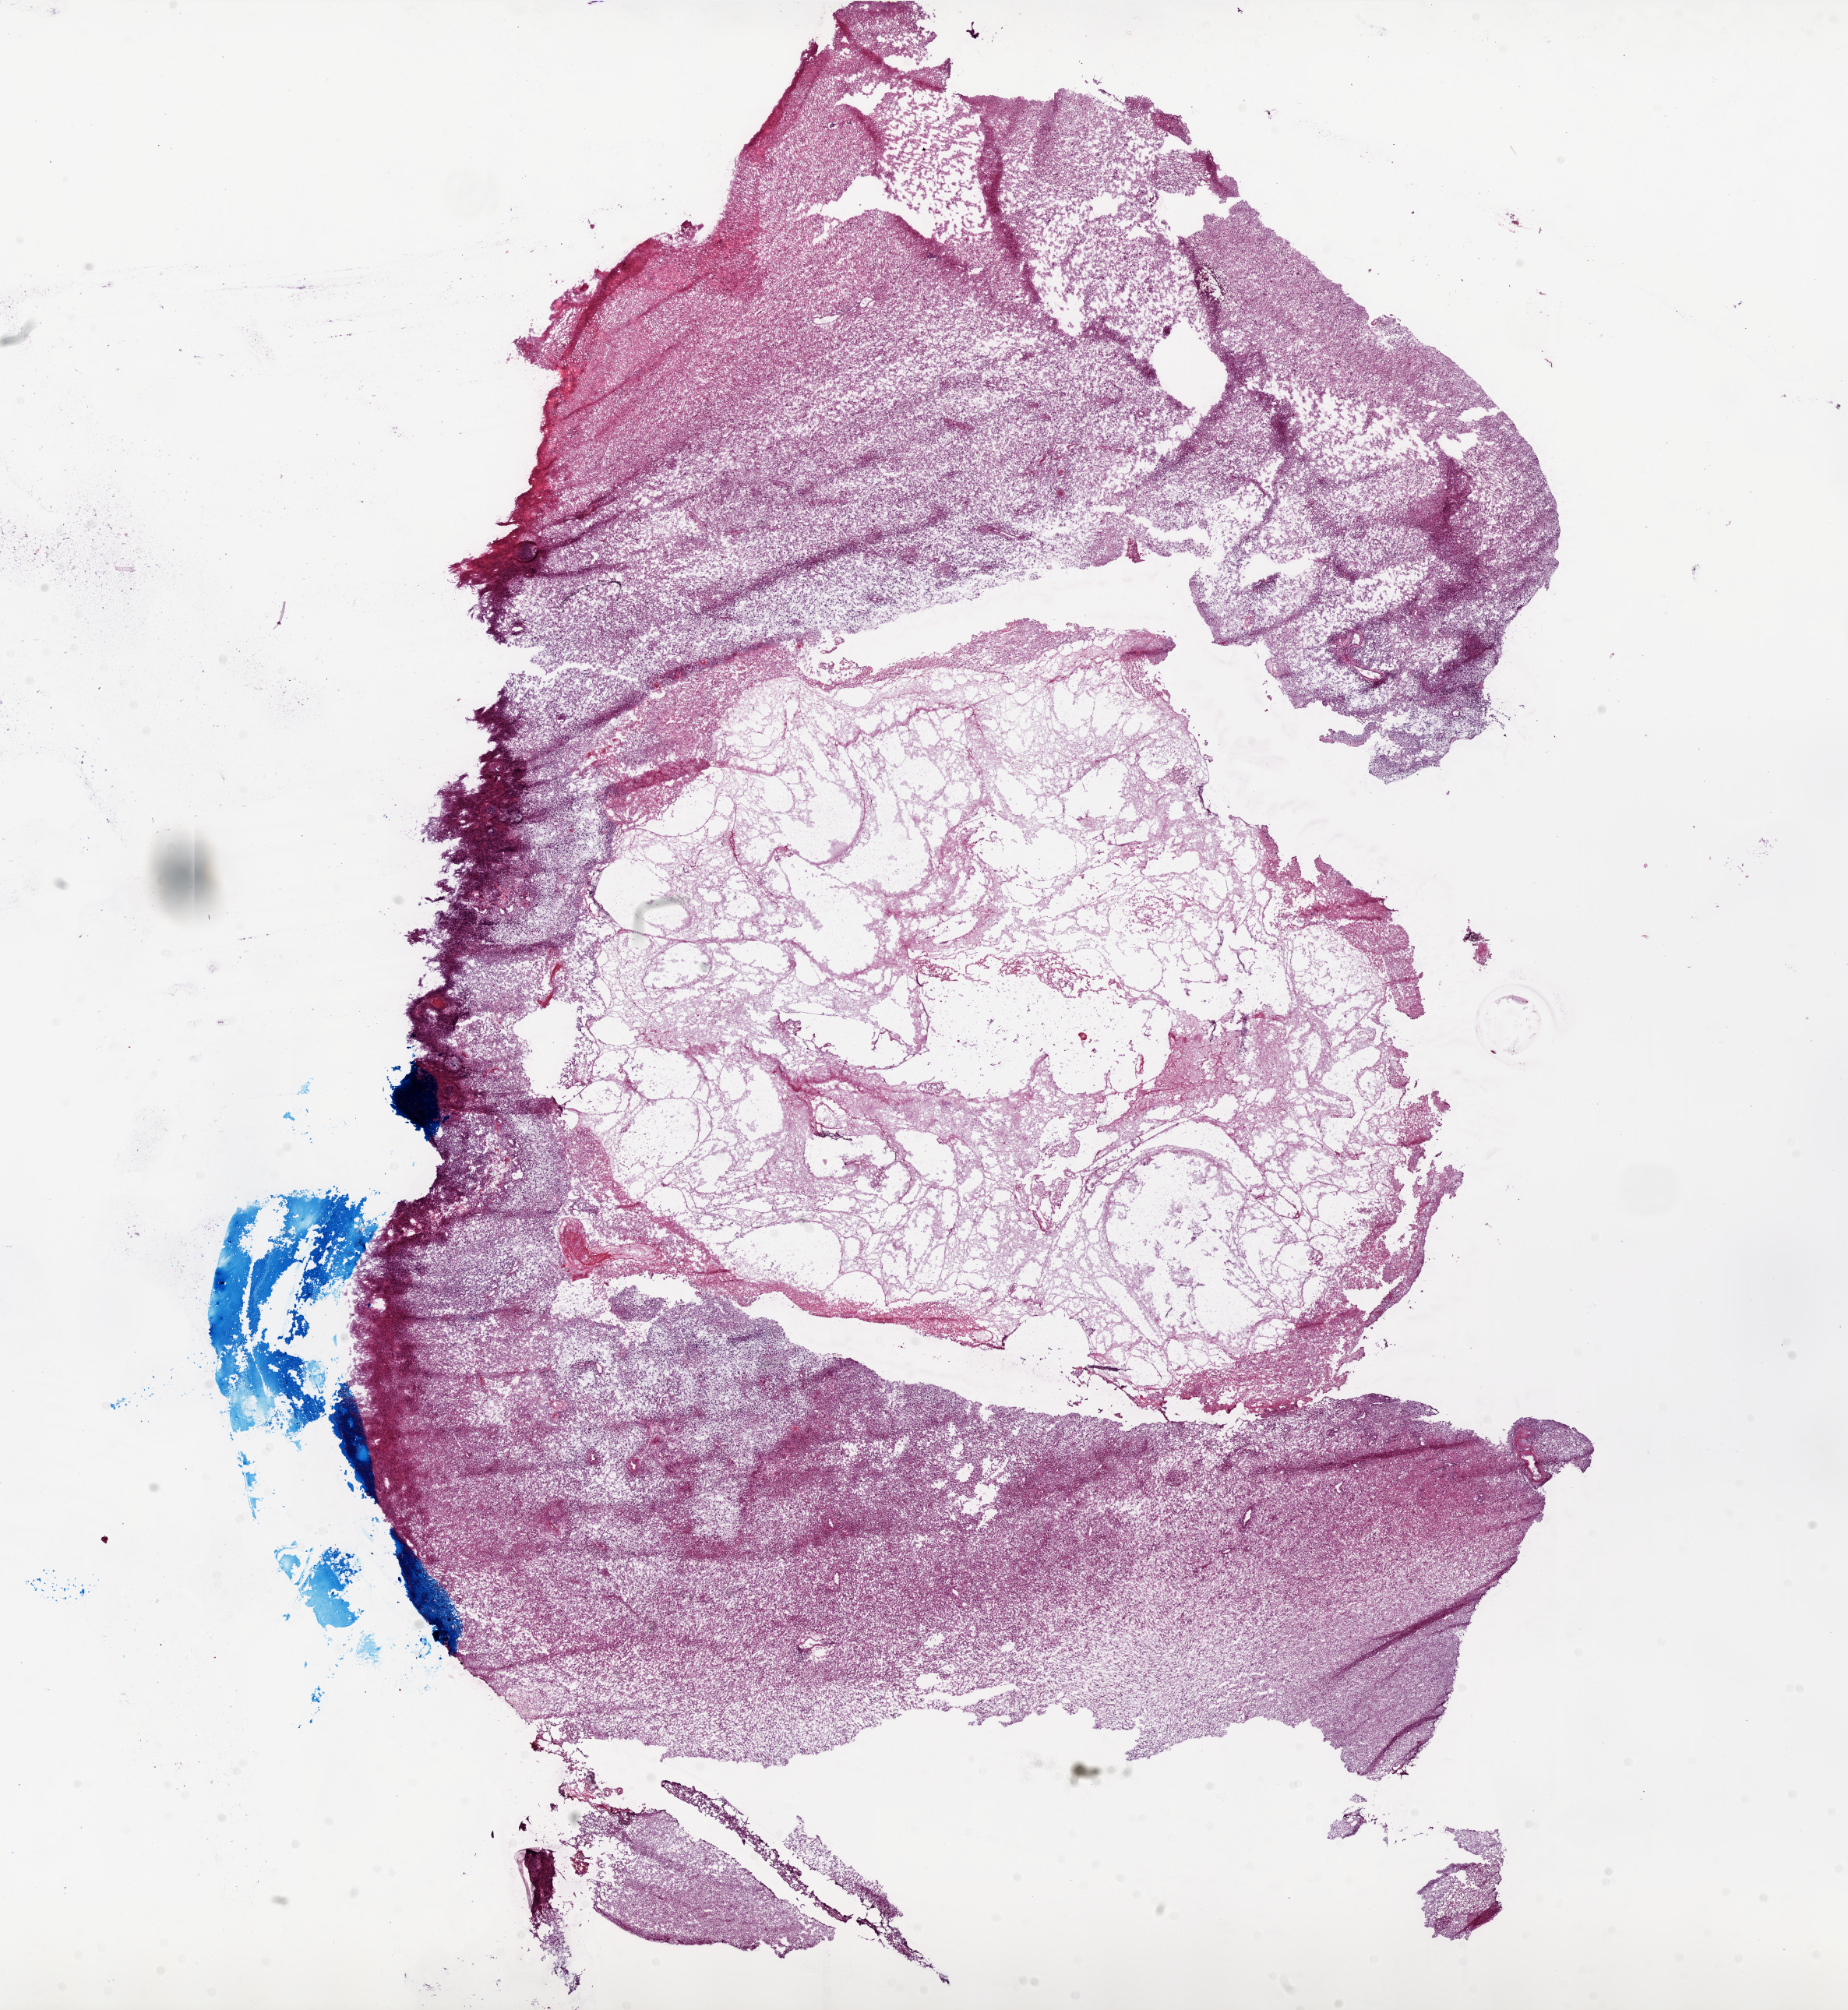
H&E-stained whole-slide image — whole scanned area (about 19.0 x 20.6 mm) shown as a low-resolution overview. Frozen section from the top of the tissue portion. Sample: primary tumour, brain. Male, age 61 years at initial diagnosis. Composition of this section per pathologist review: tumour cells 50%, tumour nuclei 90%, normal cells 0%, stromal cells 40%, necrosis 10%. Inflammatory infiltration, as recorded: lymphocyte infiltration 0%.
• histologic diagnosis: Glioblastoma